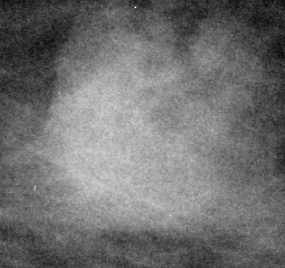
Cropped region of a digitized screen-film mammogram centred on a radiologist-marked abnormality, left breast, CC view.
Marked abnormality: mass, shape lobulated, margins ill defined; BI-RADS assessment category 4; subtlety rating 4 on a 1 (subtle) to 5 (obvious) scale; pathology (as recorded): malignant.